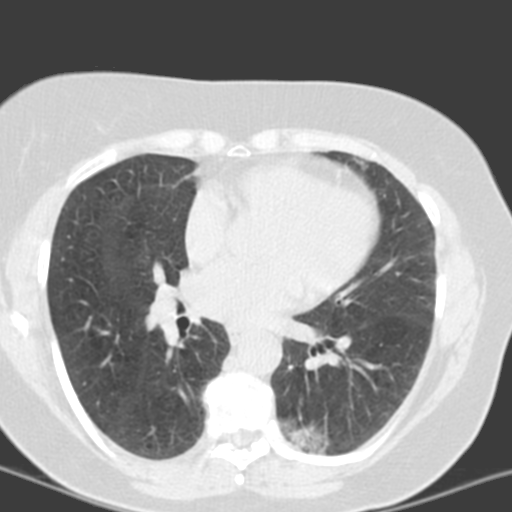
Chest CT (low-dose screening protocol), one axial image; third screening round (two years after baseline); lung window (W 1500 / L -600 HU); 3.2 mm slice thickness; standard (soft-tissue) reconstruction kernel (B); 512 × 512 image matrix, field of view 290 × 290 mm. Female, age 55 years at enrolment. Current smoker at enrolment.
Expert-annotated lung lesion, bounding box [x1, y1, x2, y2] px = [277, 404, 359, 461]. The screening reader recorded 6 non-calcified nodules or masses ≥4 mm on this exam; which of them this box marks is not recorded. Official screen result: positive, no significant change: stable abnormalities potentially related to lung cancer, unchanged since the prior screening exam.